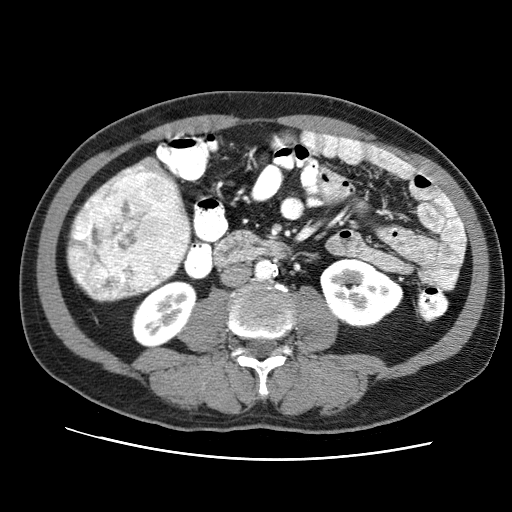
Contrast-enhanced abdominal CT (liver protocol), one axial slice. Slice 15 of 71 in the series (ordered by position). Reconstruction kernel STANDARD. 120 kVp. Soft-tissue window (W 400 / L 40 HU). 2.5 mm slice thickness. 512 × 512 image matrix, field of view 360 × 360 mm. From the clinical record (not read from this slice): diagnosis: hepatocellular carcinoma (patient treated with transarterial chemoembolisation; whether this scan precedes or follows treatment is not stated here); TNM stage (as recorded): Stage-II; Child-Pugh class: A; tumour differentiation: well differentiated; tumour nodularity: multinodular.
Annotated regions visible in this slice (semi-automatic segmentation, software-assisted and operator-edited):
- liver parenchyma outside the tumour (the mass and vessels are separate outlines, so this box may not span the whole liver): bounding box (x1, y1, x2, y2) in pixels: (66, 156, 189, 301)
- mass: (66, 165, 190, 301)
- liver vessels: (113, 177, 120, 182)